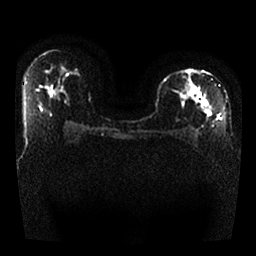
Breast MRI, one axial slice. Slice 15 of 25 in the series (ordered by position). Diffusion-weighted series; image 2 of 4 stored at this slice position (different b-values; order by instance number). 1.5 T. 4 mm slice thickness. 256 × 256 image matrix. Female patient.
Annotated regions visible in this slice (expert manual segmentation):
- tumour on diffusion-weighted imaging: bounding box <179,83,211,117> (left, top, right, bottom; pixels)